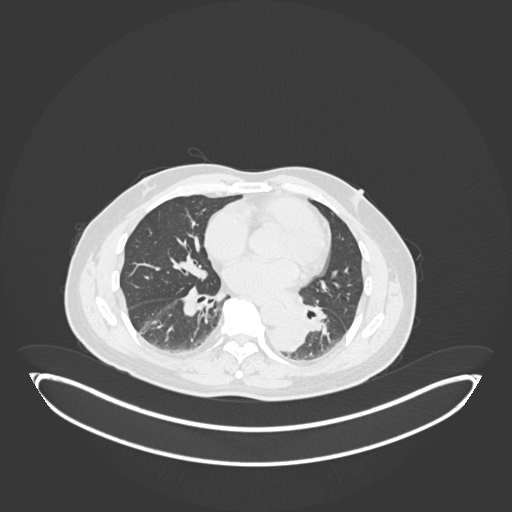
Chest CT, one axial slice. Position 83 of 258 along the scan axis. Reconstruction kernel B30f. 120 kVp. Lung window (W 1500 / L -600 HU). 1 mm slice thickness. 512 × 512 image matrix, field of view 500 × 500 mm. Male patient, age 54 years. From the clinical record (not read from this slice): clinical TNM (as recorded): T3 N0 M0.
Outlined on this slice (rectangle marked by the reading radiologist):
- lung tumour (recorded histology: squamous cell carcinoma): bounding box (x1, y1, x2, y2) in pixels: (267, 311, 309, 353)